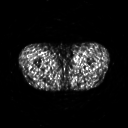
FDG PET of an extremity soft-tissue mass (from a PET/CT study), one axial slice. Slice 259 of 311 in the series (ordered by position). 3.27 mm slice thickness. 128 × 128 image matrix. Male patient, age 29 years. From the clinical record (not read from this slice): histological type: mixoid liposarcoma; grade: low; site of the primary tumour: left thigh.
Structures marked on this image (expert contour drawn on MRI and transferred to this co-registered scan by the dataset authors):
- gross tumour volume (mass): bounding box [x1, y1, x2, y2] px = [72, 56, 82, 65]